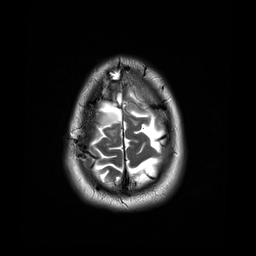
Brain MRI from a brain-tumour surgery series, one axial slice; position 6 of 44 along the scan axis; 256 × 256 image matrix, field of view 240 × 240 mm. Case-level facts recorded for this patient, not image findings: histopathology: Astrocytoma; WHO grade: 4; IDH mutation: yes.
Outlined on this slice (manually delineated by an expert):
- tumour: bounding box <94,111,121,147> (left, top, right, bottom; pixels)